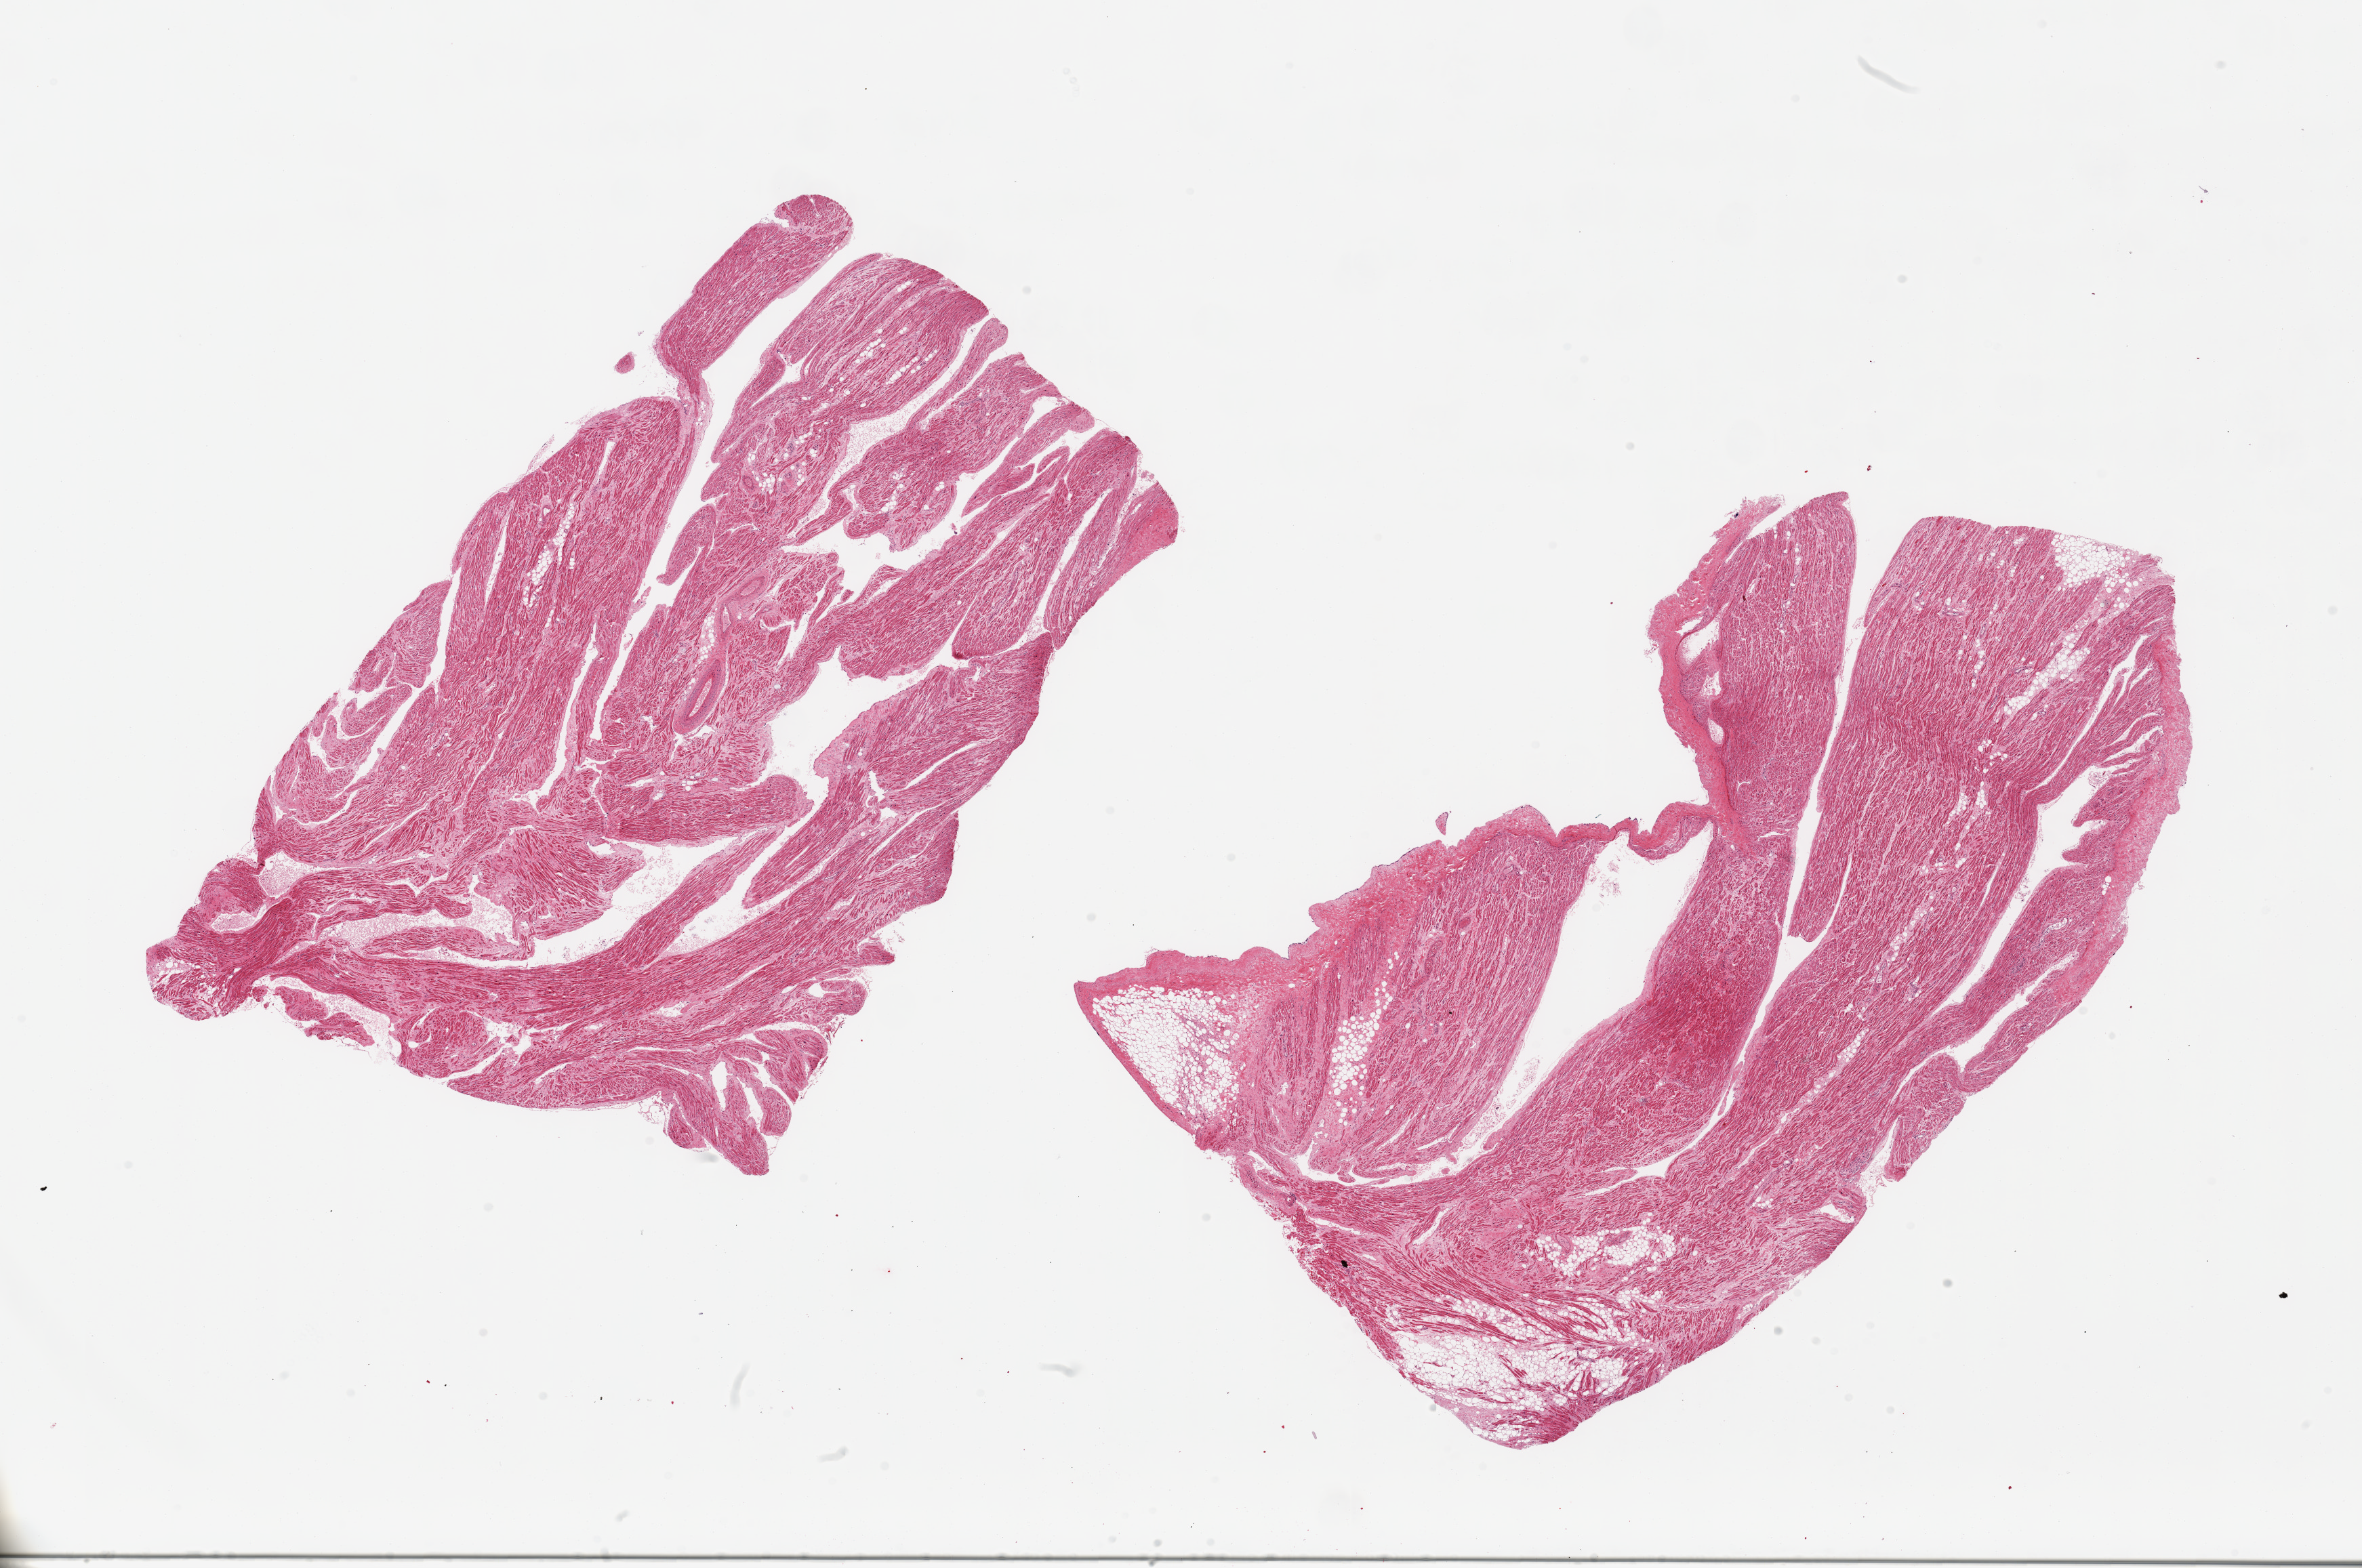
Hematoxylin and eosin (H&E) whole-slide image, shown as a low-resolution overview of the whole scanned area (about 27.6 x 18.3 mm); PAXgene-fixed paraffin-embedded (PFPE) section; sampled site (target tissue): auricular appendage; donor tissue sample. Donor: male.
• pathologist's review note for this sample: 2 pieces; 1 includes up to 15% fat